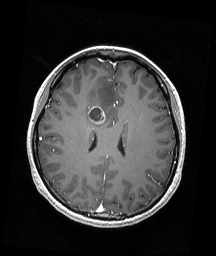
Brain MRI from a brain-tumour surgery series, one axial slice; position 74 of 192 along the scan axis; T1-weighted post-contrast; 1 mm slice thickness; 216 × 256 image matrix. Case-level facts recorded for this patient, not image findings: histopathology: Astrocytoma; WHO grade: 4; IDH mutation: yes; tumour location: Right Frontal.
Annotated regions visible in this slice (outlined manually by an expert reader):
- tumour: bounding box <87,106,105,124> (left, top, right, bottom; pixels)